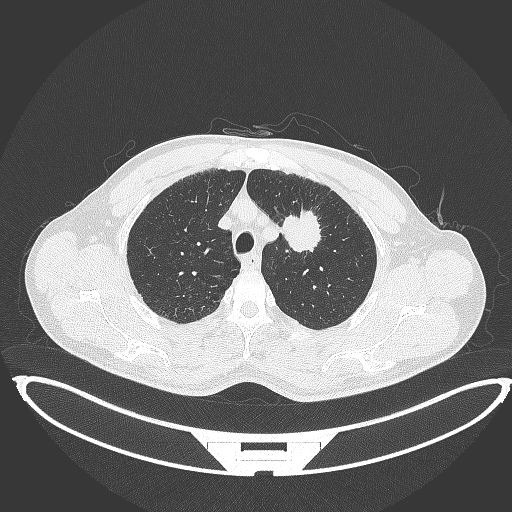
Chest CT, one axial slice. Slice 349 of 395 in the series (ordered by position). Lung window (W 1500 / L -600 HU). 1 mm slice thickness. 512 × 512 image matrix, field of view 457 × 457 mm. Male patient, age 60 years. Case-level facts recorded for this patient, not image findings: clinical TNM (as recorded): T2a N0 M0; histopathological grade: G1-G2.
Structures marked on this image (bounding box drawn by a radiologist):
- lung tumour (recorded histology: squamous cell carcinoma): bounding box <282,204,321,255> (left, top, right, bottom; pixels)